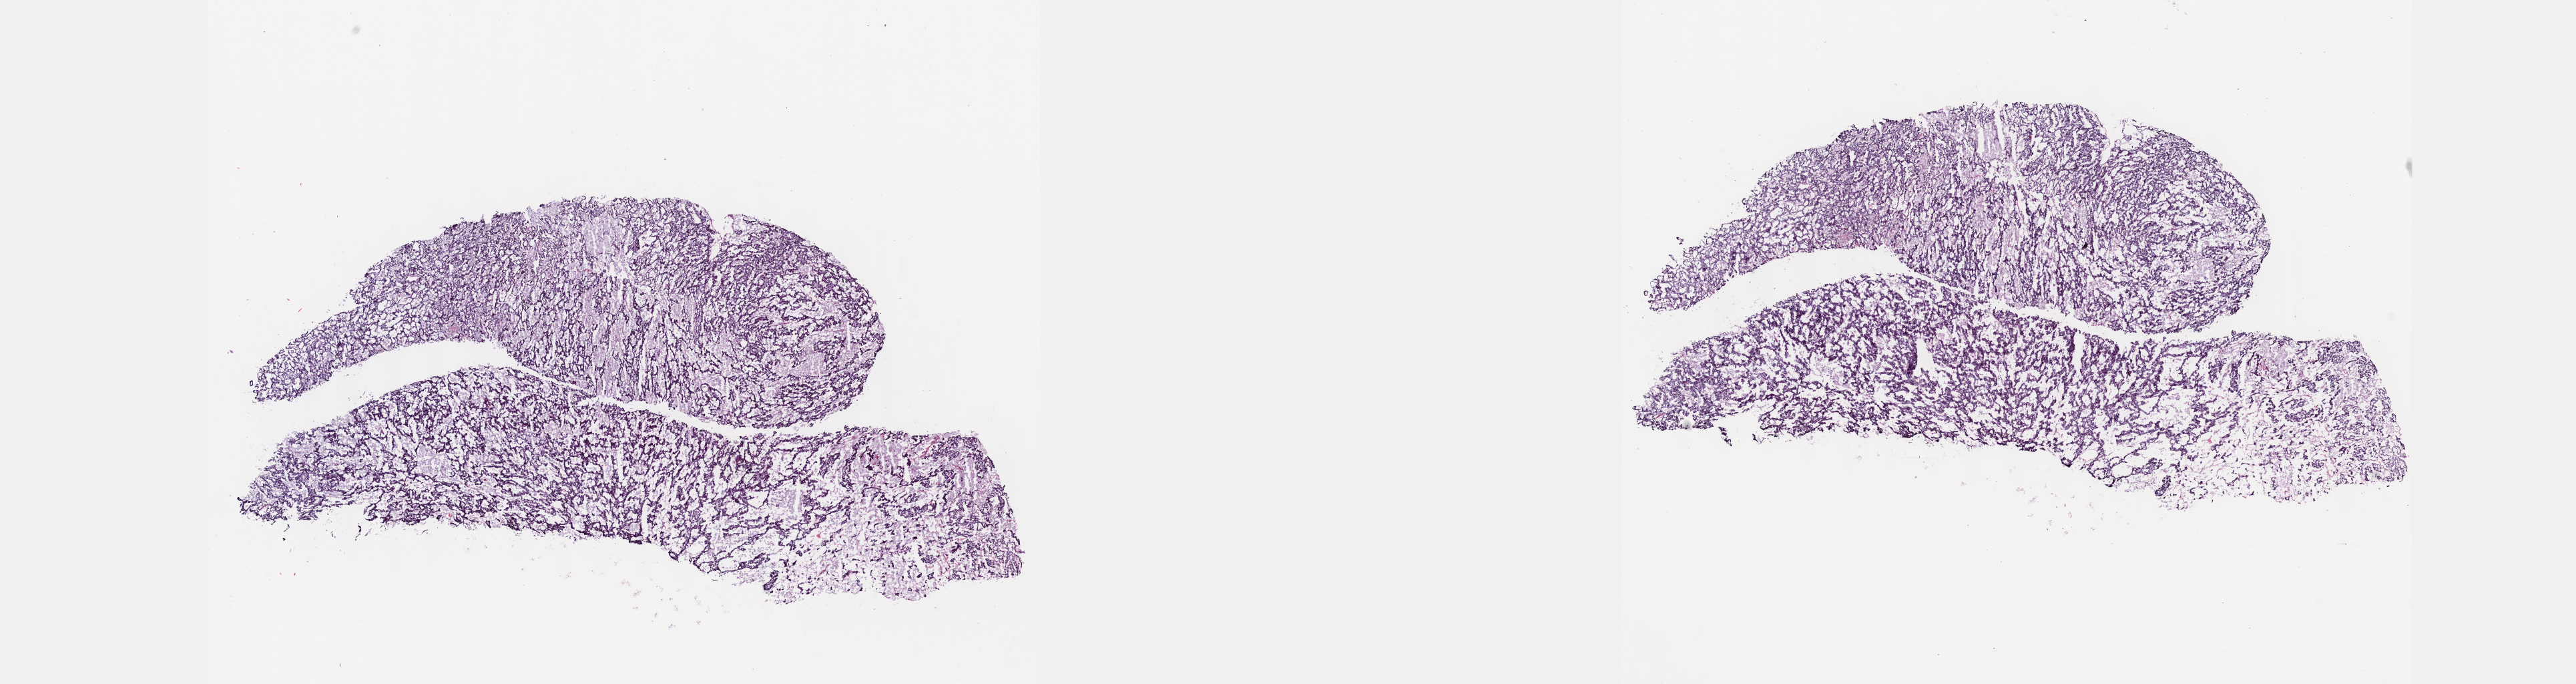
Digitized Hematoxylin and eosin (H&E) stained tissue section (whole slide) — shown as a low-resolution overview of the whole scanned area (about 31.2 x 8.3 mm, slide scanned at 40x), frozen section, sample: primary tumour, kidney. Male patient; age at initial diagnosis 52 years. Slide review estimates, as recorded: tumour cells 60%, tumour nuclei 70%, normal cells 0%, stromal cells 40%, necrosis 0%. Infiltration values recorded for this section: lymphocyte infiltration 0%, monocyte infiltration 0%, neutrophil infiltration 0%.
* laterality: right
* diagnosis: Papillary adenocarcinoma, NOS
* AJCC pathologic stage: I (7th edition)